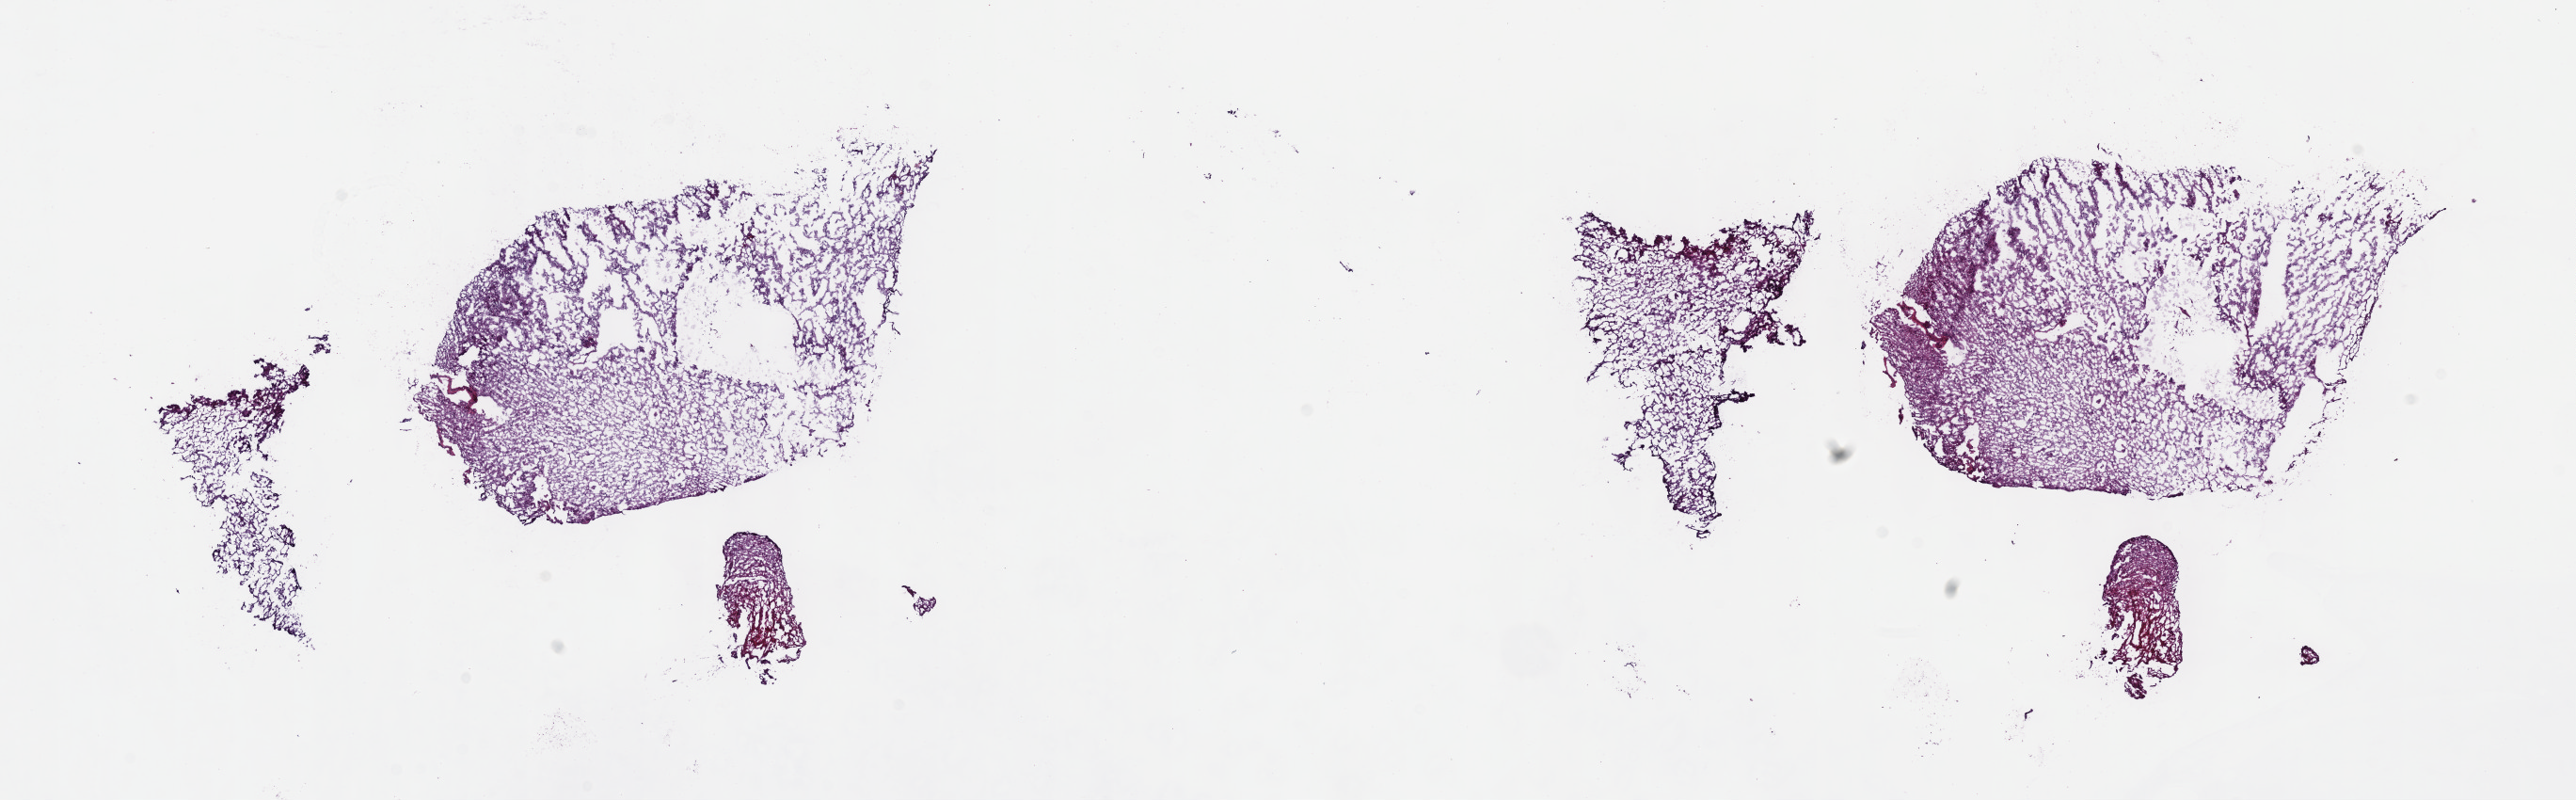
Digitized H&E-stained tissue section (whole slide) — a low-resolution overview of the entire scanned area, about 22.1 x 6.9 mm (acquisition: 40x scan). Frozen section from the top of the tissue portion. Brain, primary tumour sample. Female patient; age at initial diagnosis 32 years. Histologic grade: G3 (poorly differentiated). Pathologist review of this section (percent, as recorded): tumour cells 25%, tumour nuclei 70%, normal cells 10%, stromal cells 65%, necrosis 0%. Inflammatory infiltration, as recorded: lymphocyte infiltration 0%, monocyte infiltration 0%, neutrophil infiltration 0%.
* pathologic diagnosis: Astrocytoma, anaplastic (cerebrum)